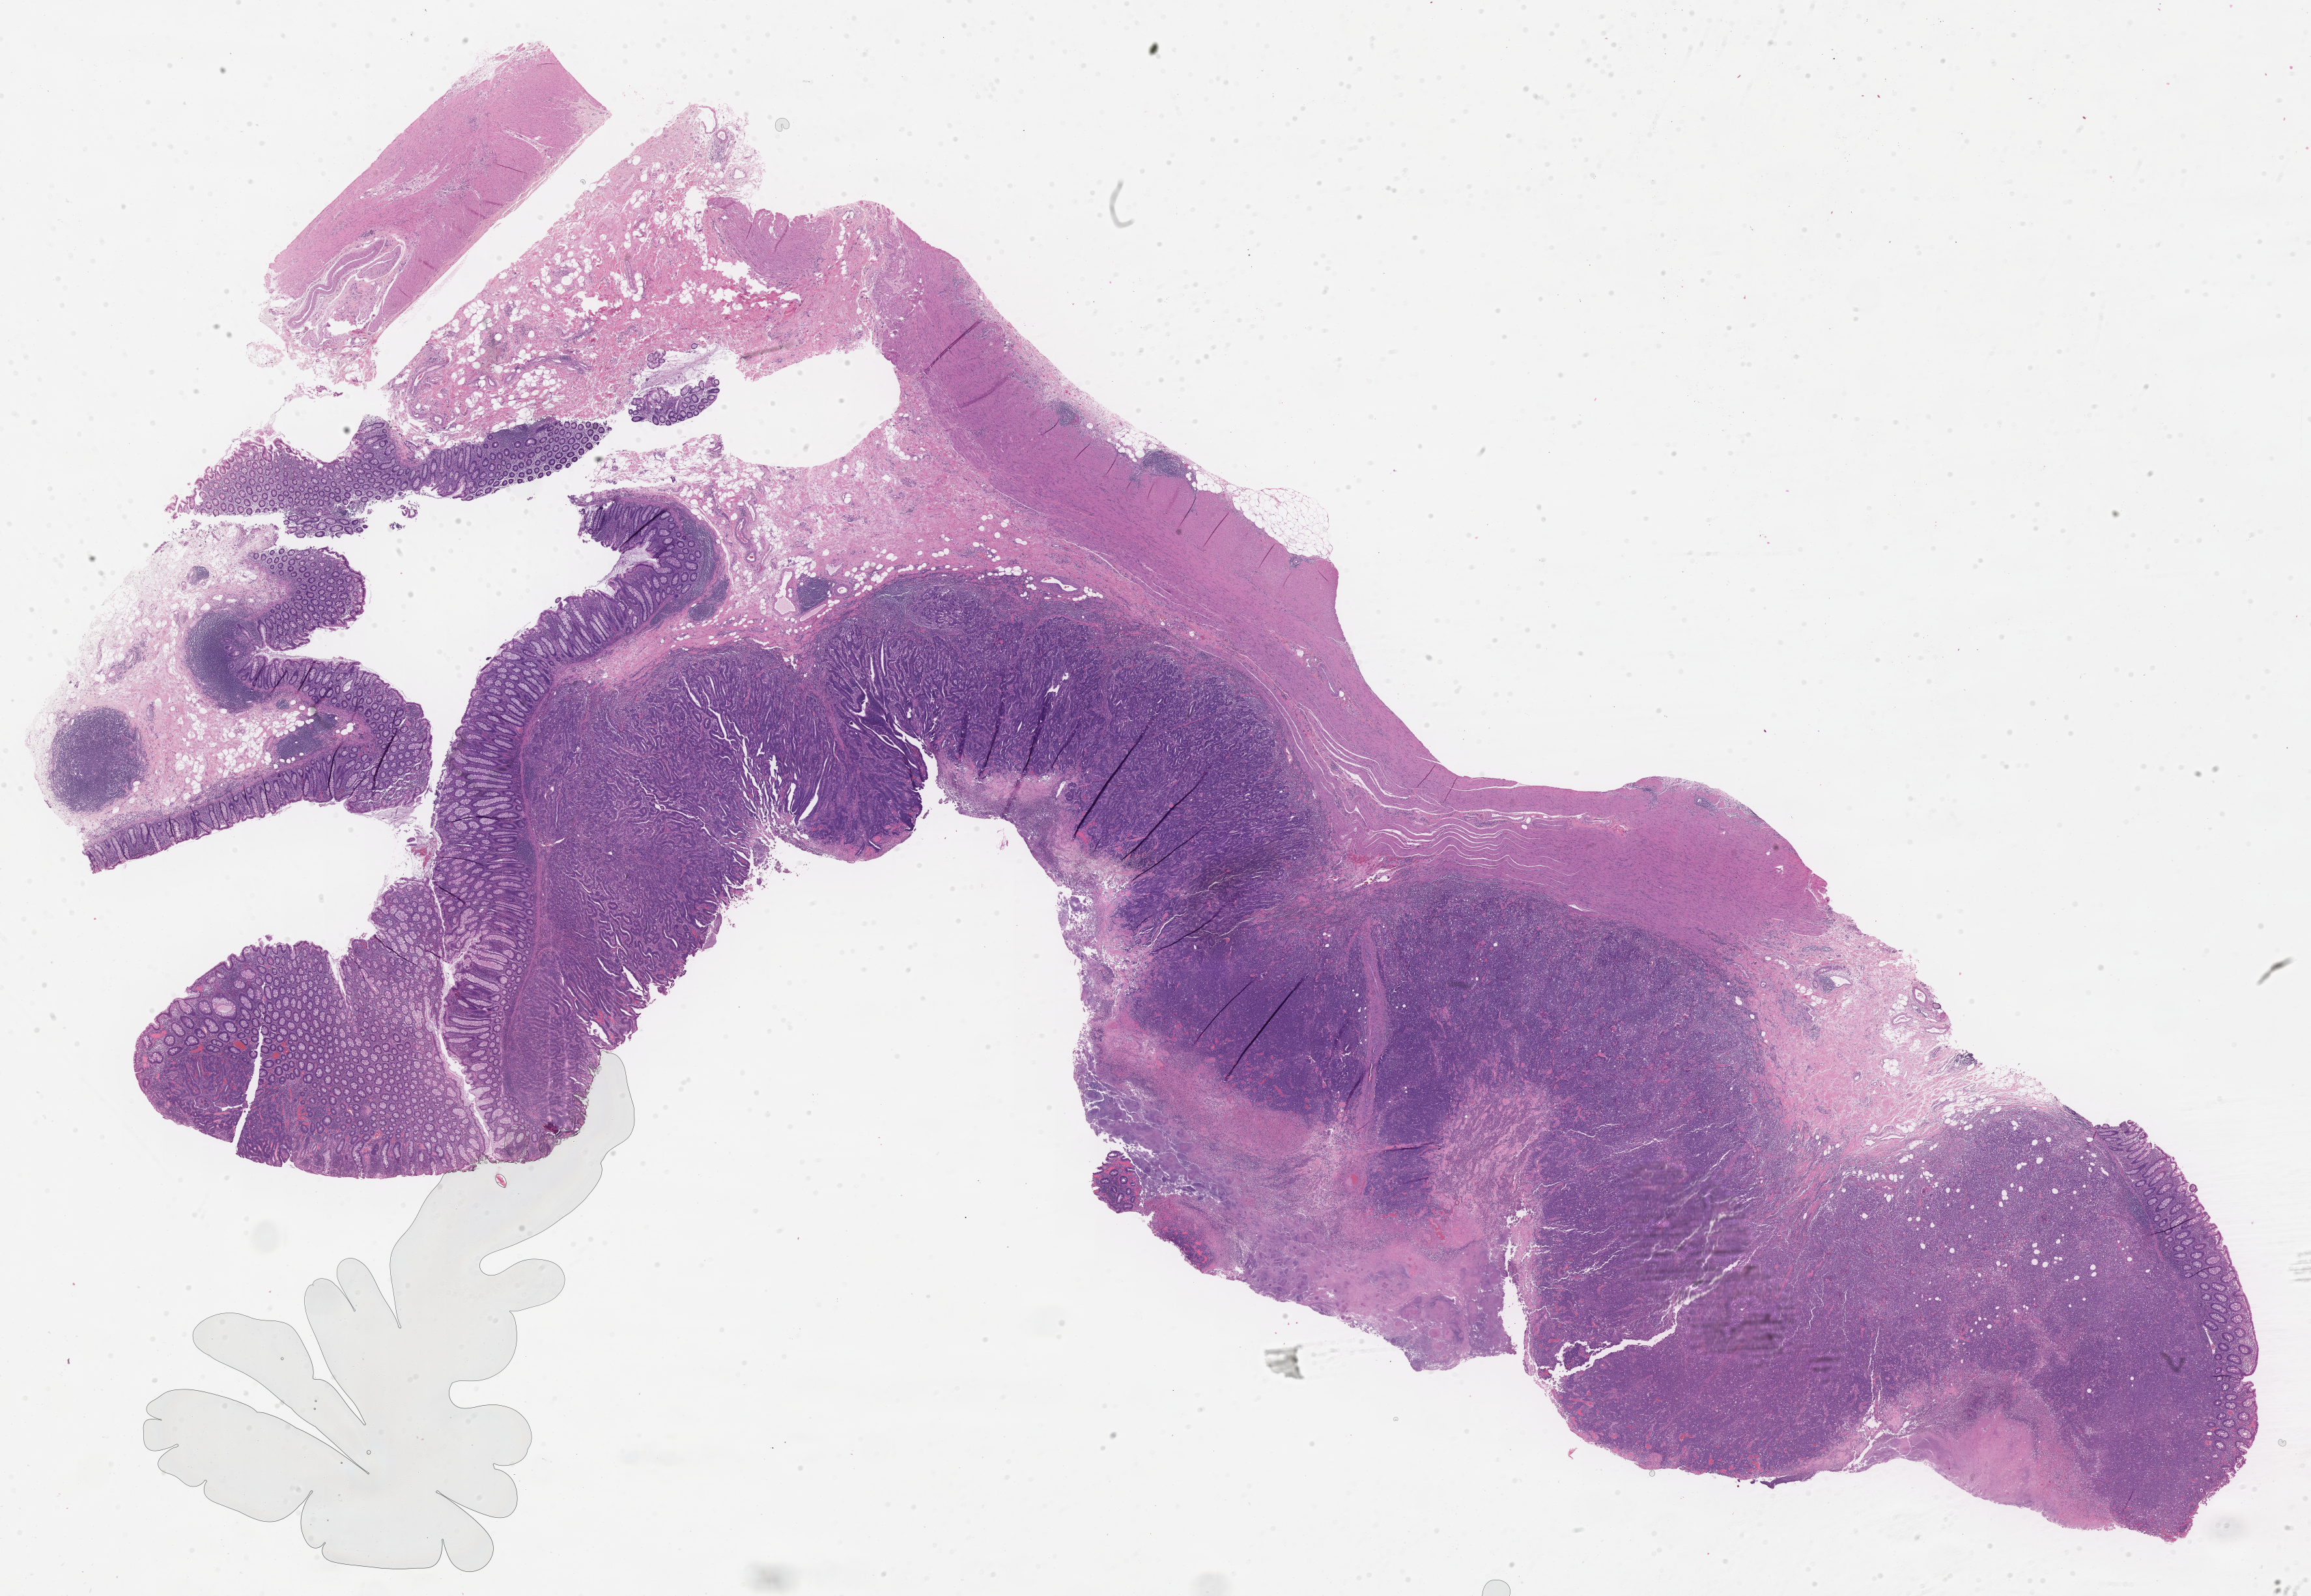
Digitized H&E-stained section, whole scanned area (about 28.6 x 19.8 mm) shown as a low-resolution overview, formalin-fixed paraffin-embedded section, specimen: primary tumor, site: ascending colon. Male patient; age at initial diagnosis 46 years. Tumor grade: G3 (poorly differentiated). Pathologist review of this section (percent, as recorded): tumor cells 50%, tumor nuclei 70%, stromal cells 0%, necrosis 0%, normal cells 50%. Inflammatory infiltration, as recorded: lymphocyte infiltration 0%, monocyte infiltration 0%, neutrophil infiltration 0%.
Section: top of the tissue portion. Diagnosis: Adenocarcinoma, NOS. AJCC pathologic stage: Stage IIA.